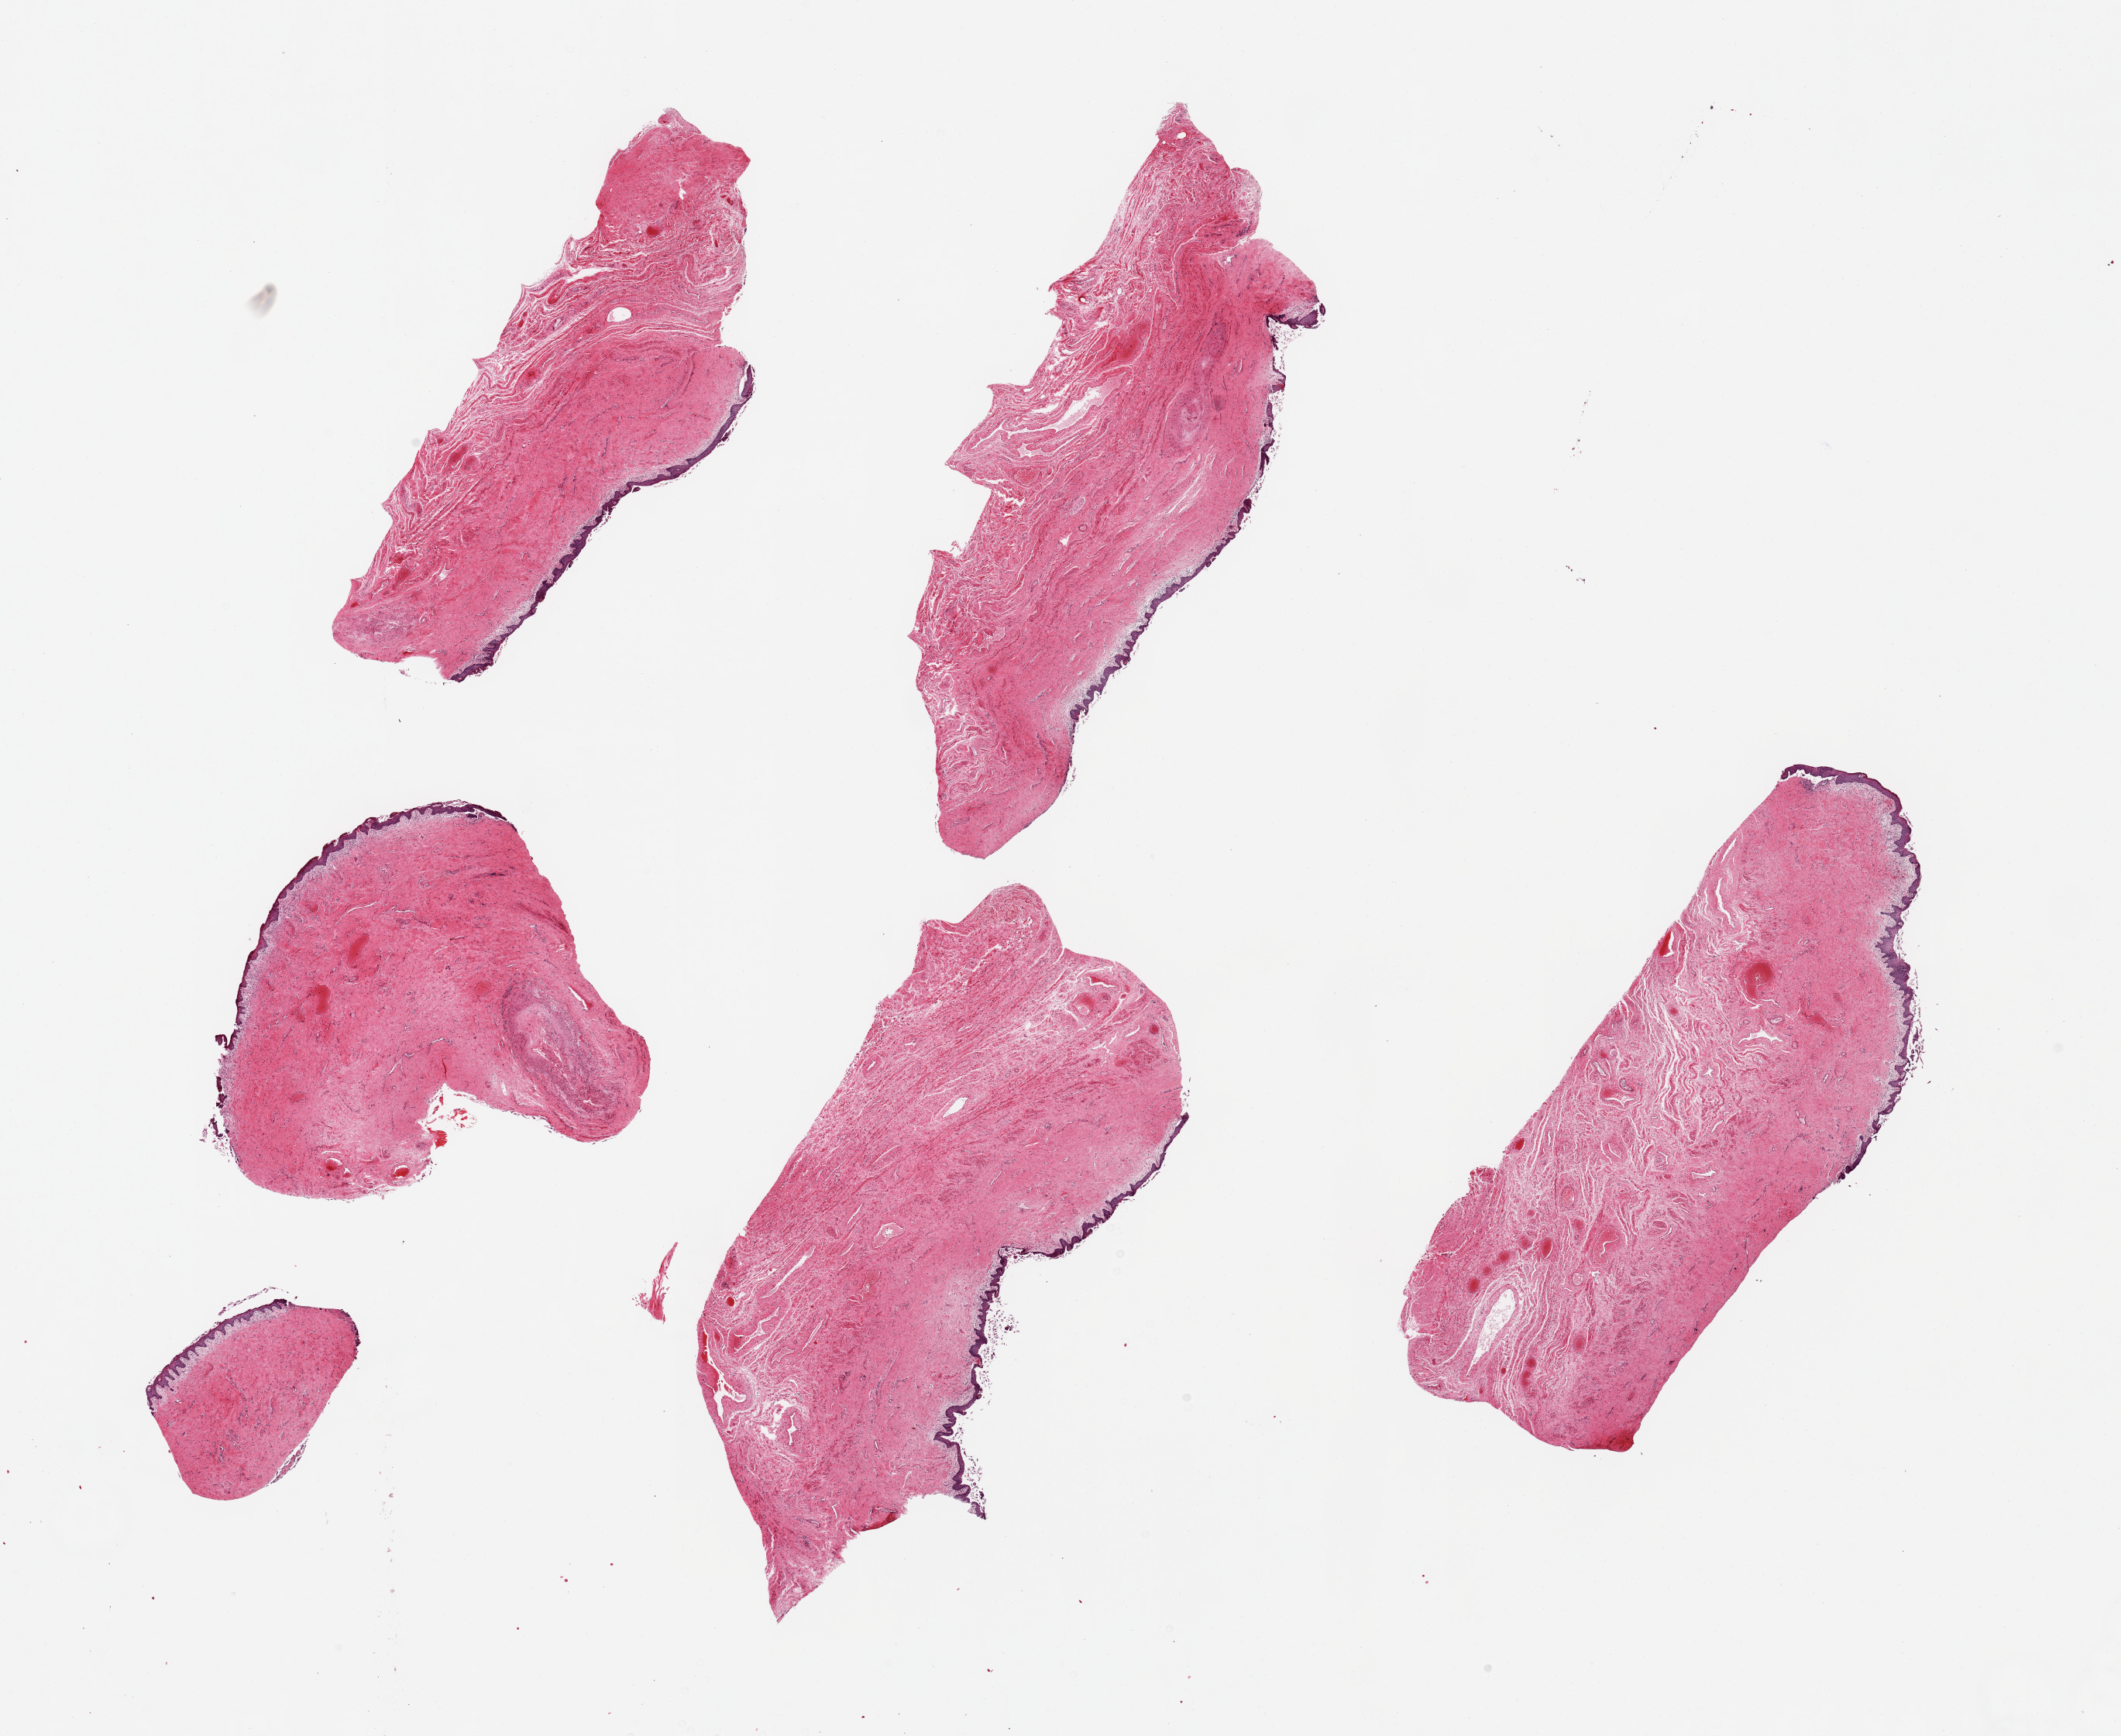
H&E whole-slide image — shown as a low-resolution overview of the whole scanned area (about 21.7 x 17.7 mm), PAXgene-fixed, paraffin-embedded tissue, sampled site (target tissue): vagina, donor tissue sample.
Reviewer comment on this tissue sample: 5 pieces, sloughing squamous mucosa up to ~0.1mm.